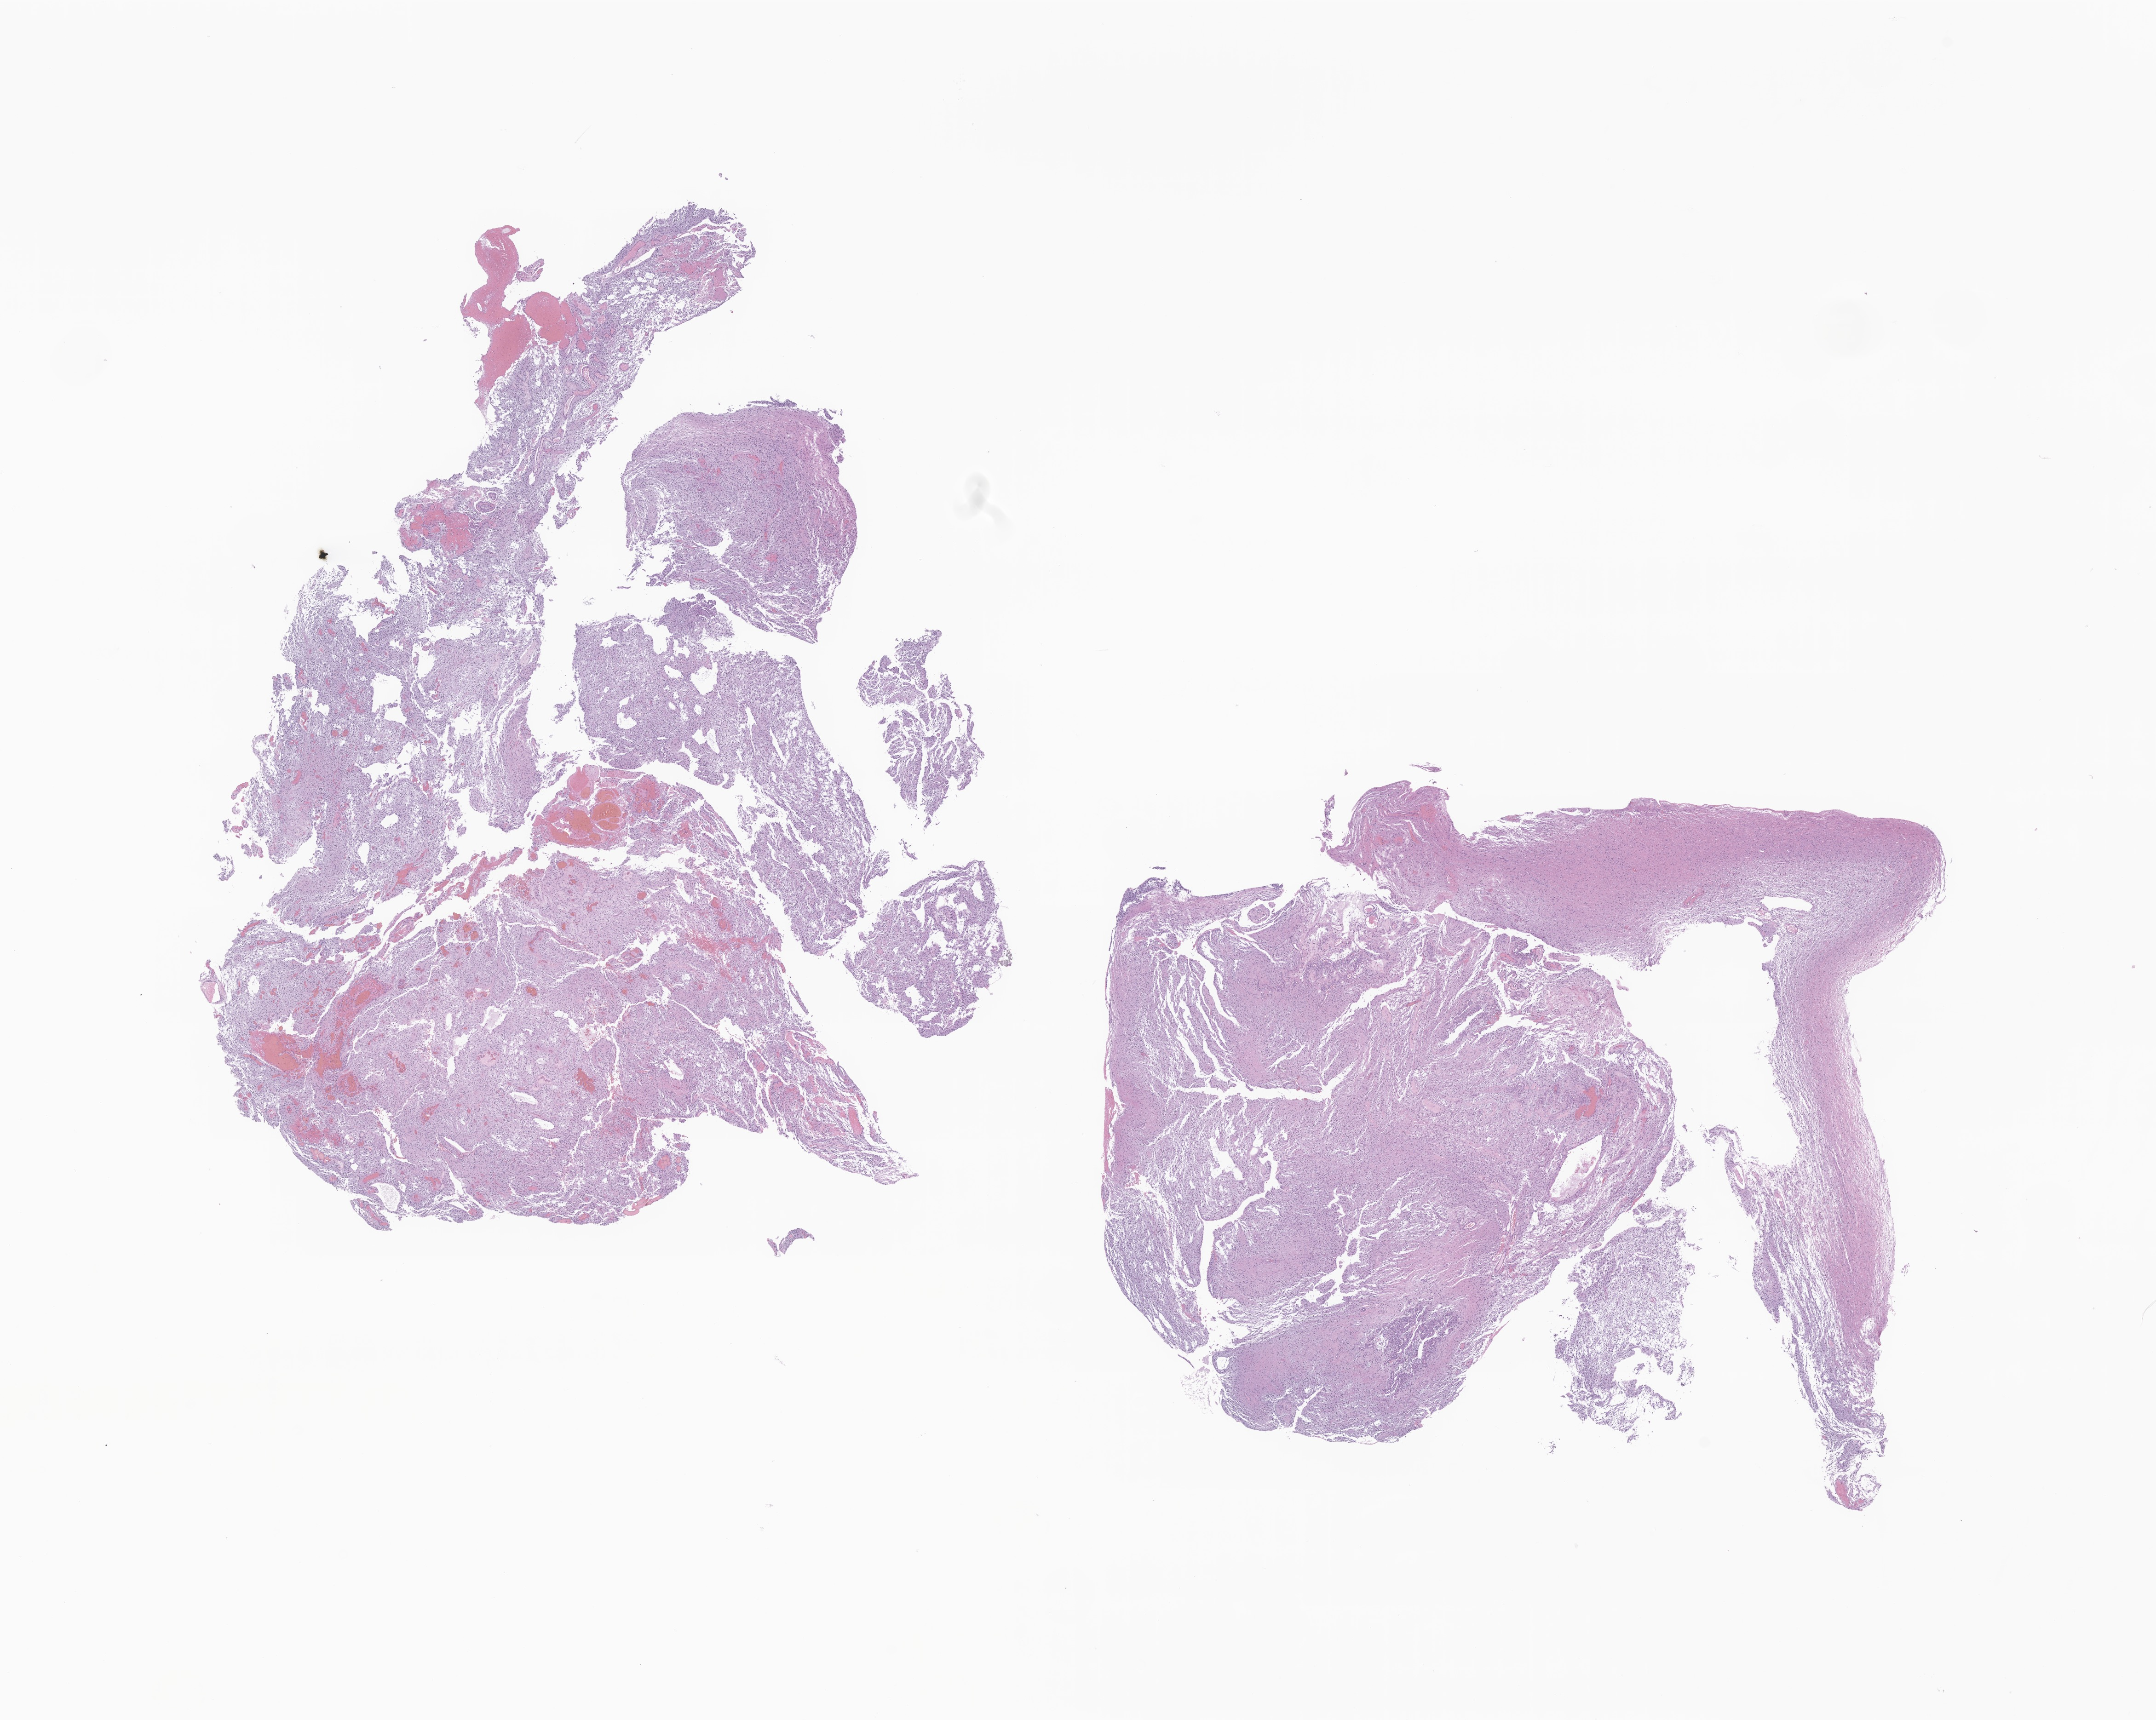
Whole-slide image, H&E stain of tumor tissue from the brain — low-resolution overview of the scanned area, about 19.8 x 15.8 mm. FFPE section. Male patient, age 59 months (4 years 11 months).
Diagnosis (ICD-O-3 morphology term): Pilocytic astrocytoma.